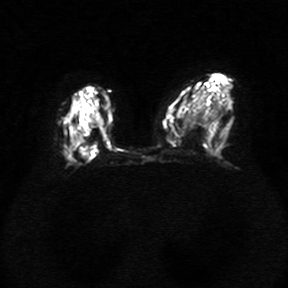
Breast MRI, one axial slice. Position 15 of 34 along the scan axis. Diffusion-weighted series; image 2 of 4 stored at this slice position (different b-values; order by instance number). 1.5 T. 5 mm slice thickness. 288 × 288 image matrix, field of view 340 × 340 mm. Female patient.
Structures marked on this image (expert manual segmentation):
- tumour on diffusion-weighted imaging: box from (x=68, y=136) to (x=91, y=160) px